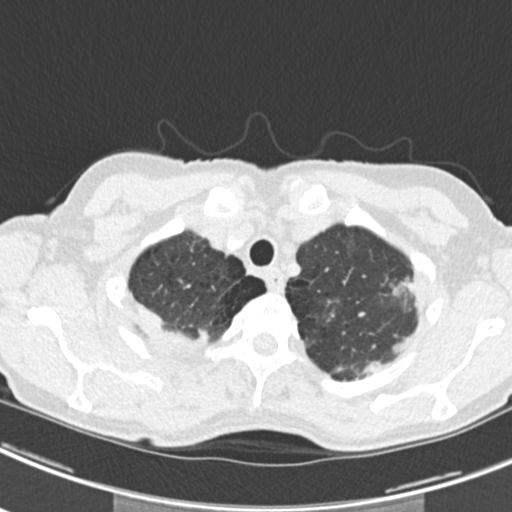
Chest CT (low-dose screening protocol), one axial image, second annual screen, lung window (W 1500 / L -600 HU), 2 mm slice thickness, slice 32 of 219 in the series. Female, age 63 years at enrolment. Current smoker at enrolment.
Expert reader's lesion annotation, bounding box (x1, y1, x2, y2) in pixels: (365, 260, 427, 319). The screening reader recorded 9 non-calcified nodules or masses ≥4 mm on this exam (left upper lobe, right upper lobe, left upper lobe, left lower lobe, right middle lobe, left lower lobe, left lower lobe, right lower lobe, right lower lobe); which of them this box marks is not recorded. Participant outcome: lung cancer diagnosed 408 days after this screen (after the third annual screen) — bronchiolo-alveolar adenocarcinoma, NOS, right upper lobe, right middle lobe, right lower lobe, left upper lobe, left lower lobe, moderately differentiated (G2), stage IV (AJCC 6th edition).